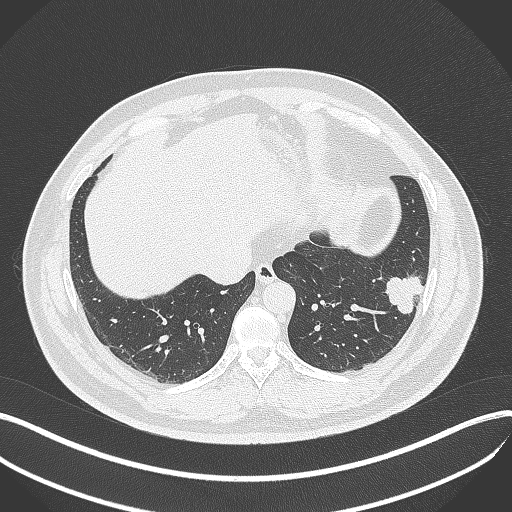
Chest CT, one axial slice. Position 121 of 429 along the scan axis. Reconstruction kernel B70f. Lung window (W 1500 / L -600 HU). 1 mm slice thickness. 512 × 512 image matrix, field of view 400 × 400 mm. Male patient, age 39 years. From the clinical record (not read from this slice): clinical TNM (as recorded): T2a N0 M0; histopathological grade: G2-3.
Annotated regions visible in this slice (rectangle marked by the reading radiologist):
- lung tumour (recorded histology: adenocarcinoma): bounding box <381,270,428,315> (left, top, right, bottom; pixels)